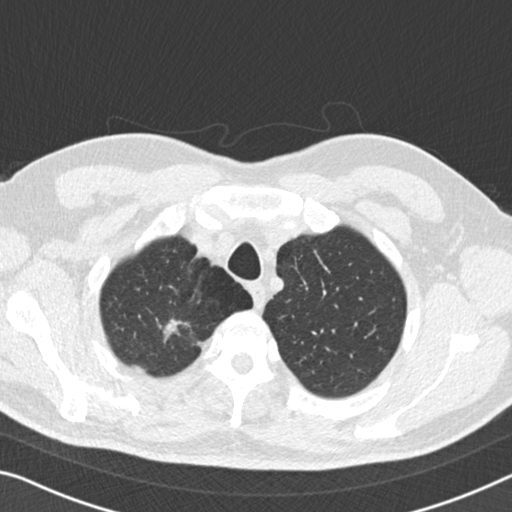
Axial slice from a low-dose chest CT screening exam. Third screening round (two years after baseline). Lung window (W 1500 / L -600 HU). 2 mm slice thickness. Standard (soft-tissue) reconstruction kernel (B30f). Slice 25 of 167 in the series. Male participant, aged 56 years at enrolment. Former smoker at enrolment.
- Lesion marked by an expert reader, bounding box [x1, y1, x2, y2] px = [145, 306, 207, 358].
- Reader record for this screening exam (exam-level; its link to the box is not recorded): non-calcified nodule or mass ≥4 mm, right upper lobe, 13 × 13 mm, spiculated (stellate) margins, soft tissue attenuation, pre-existing on the prior screen: yes; interval growth: yes.
- Later outcome: lung cancer diagnosed 97 days after this screen — adenocarcinoma, NOS, right upper lobe, moderately differentiated (G2), stage IA (AJCC 6th edition), 9 mm at pathology.